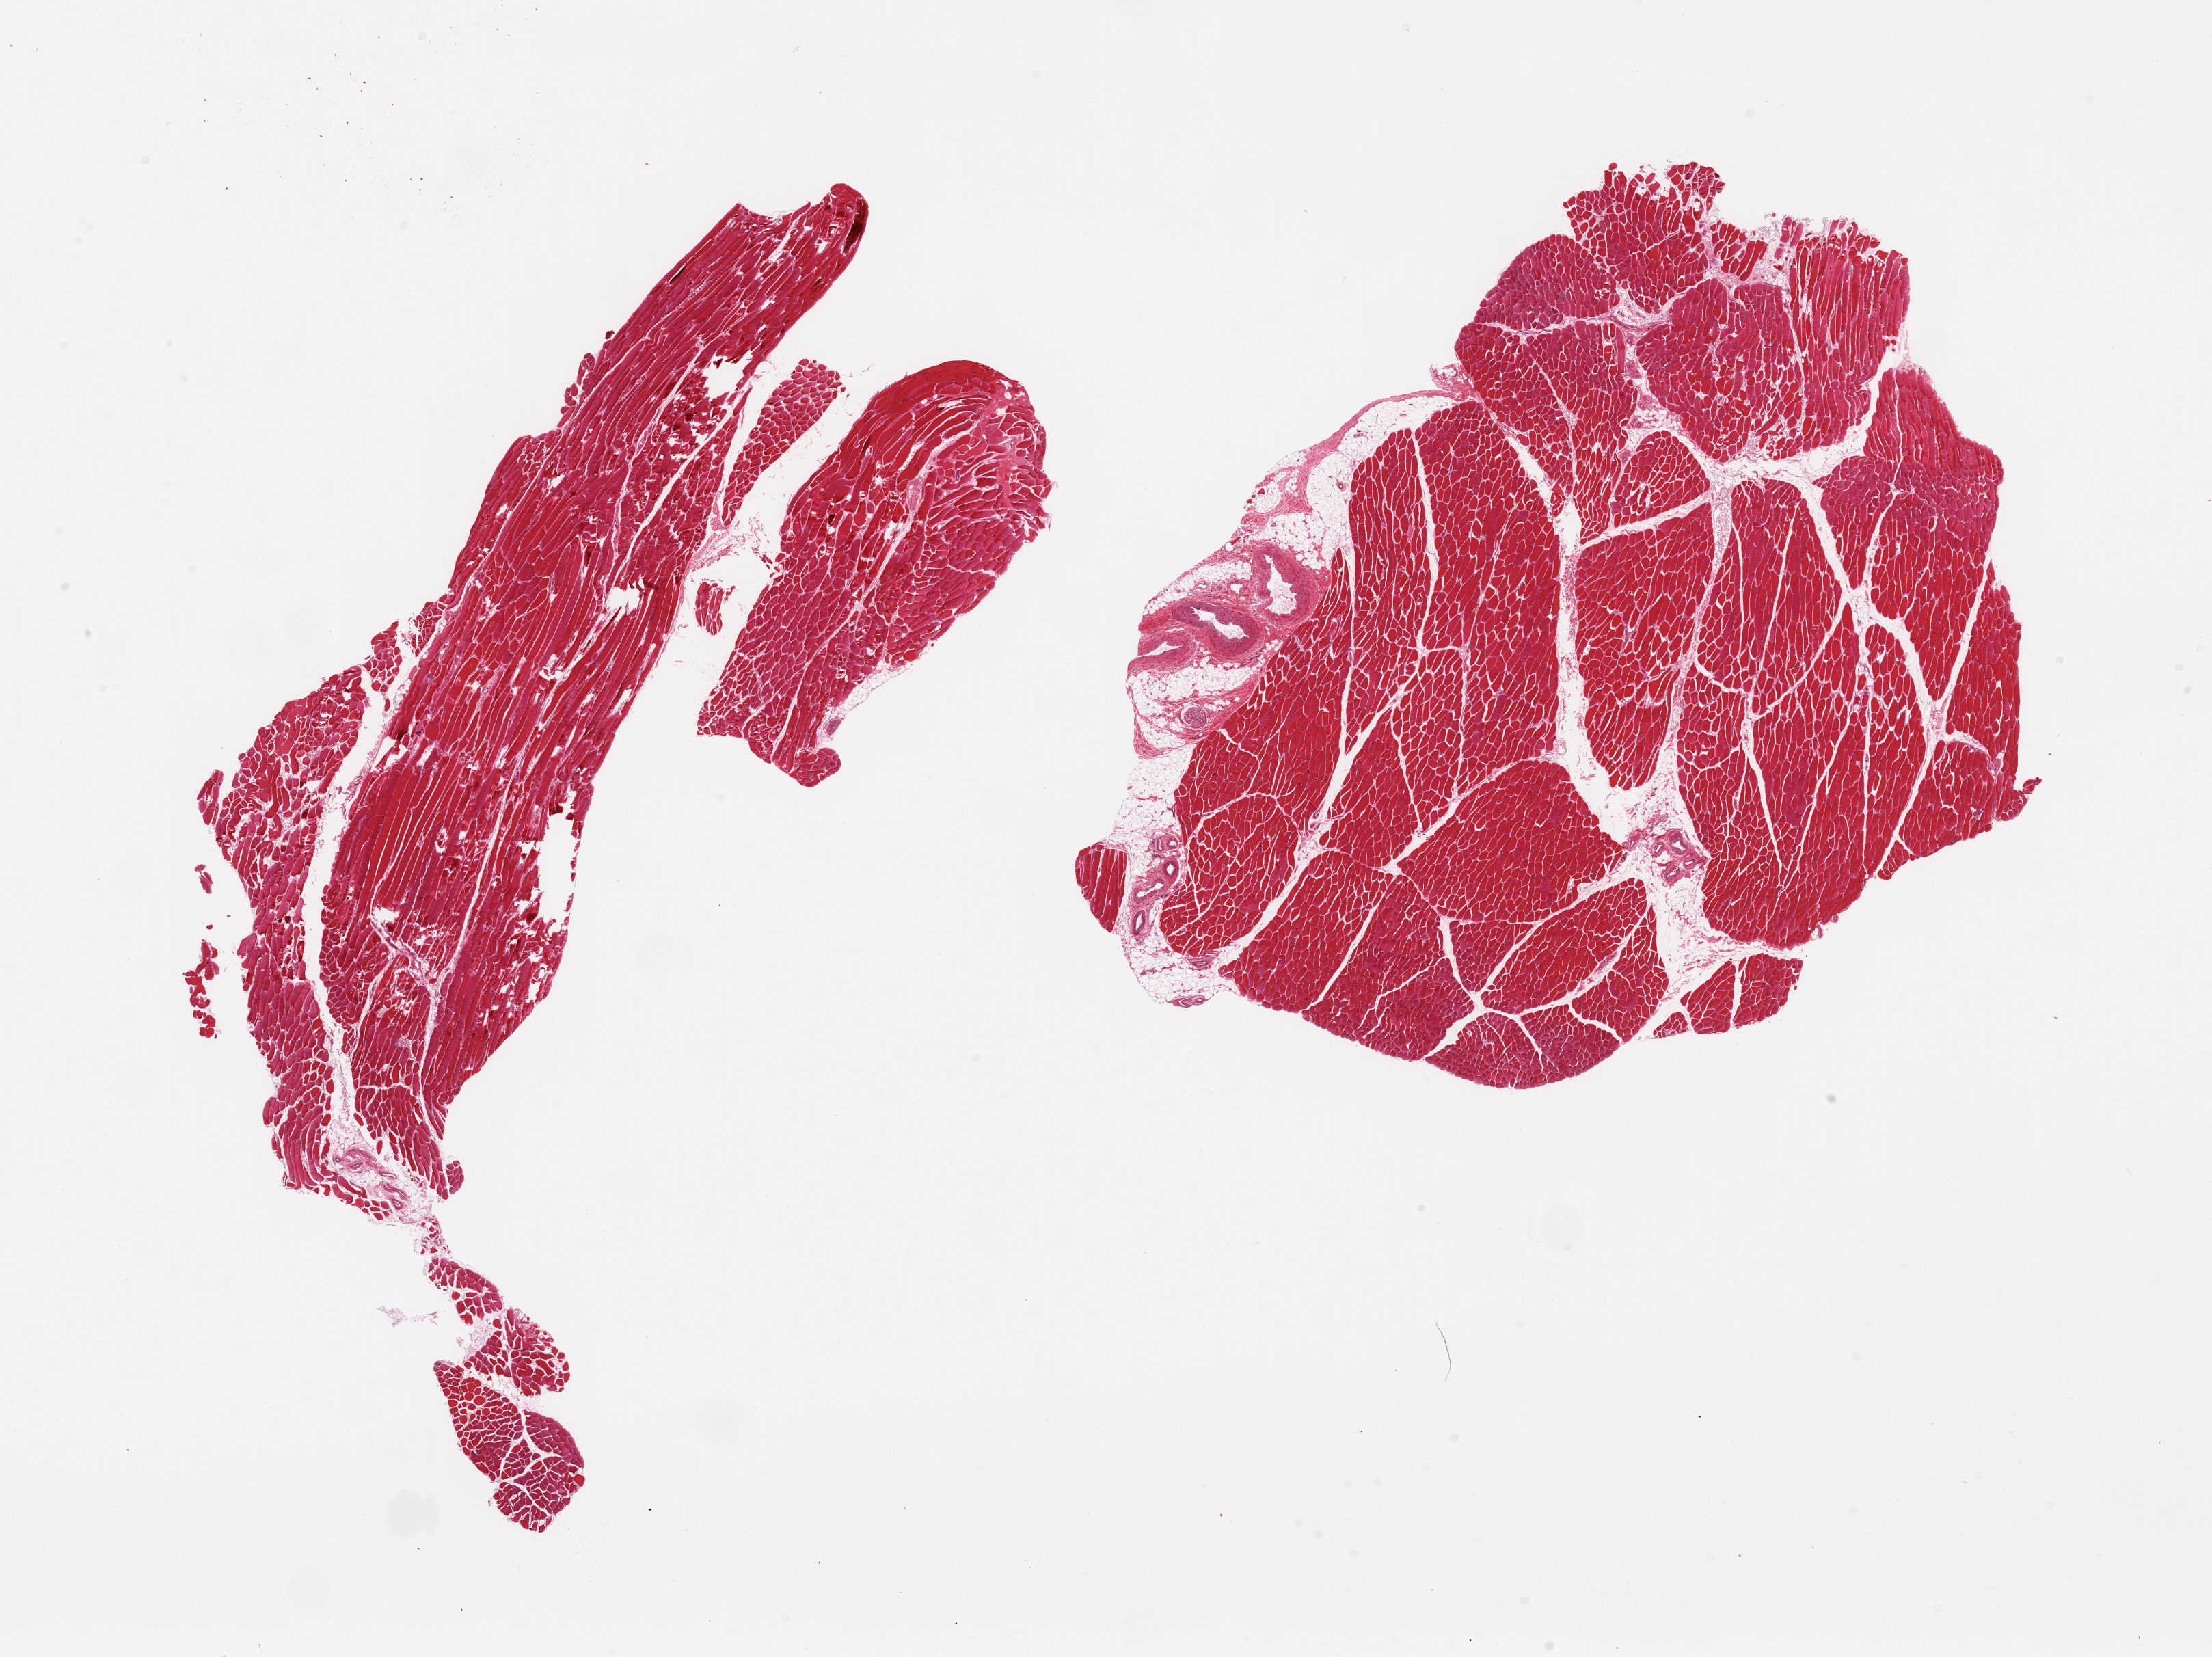
Digitized haematoxylin and eosin-stained section, brightfield — shown as a low-resolution overview of the whole scanned area (about 25.6 x 19.2 mm, acquisition: 20x scan), PAXgene-fixed paraffin-embedded (PFPE) section, section of skeletal muscle (target tissue), donor tissue sample. Donor sex: male.
- reviewer comment on this tissue sample: 2 pieces adherent; interstitital fat is ~10% of tissue